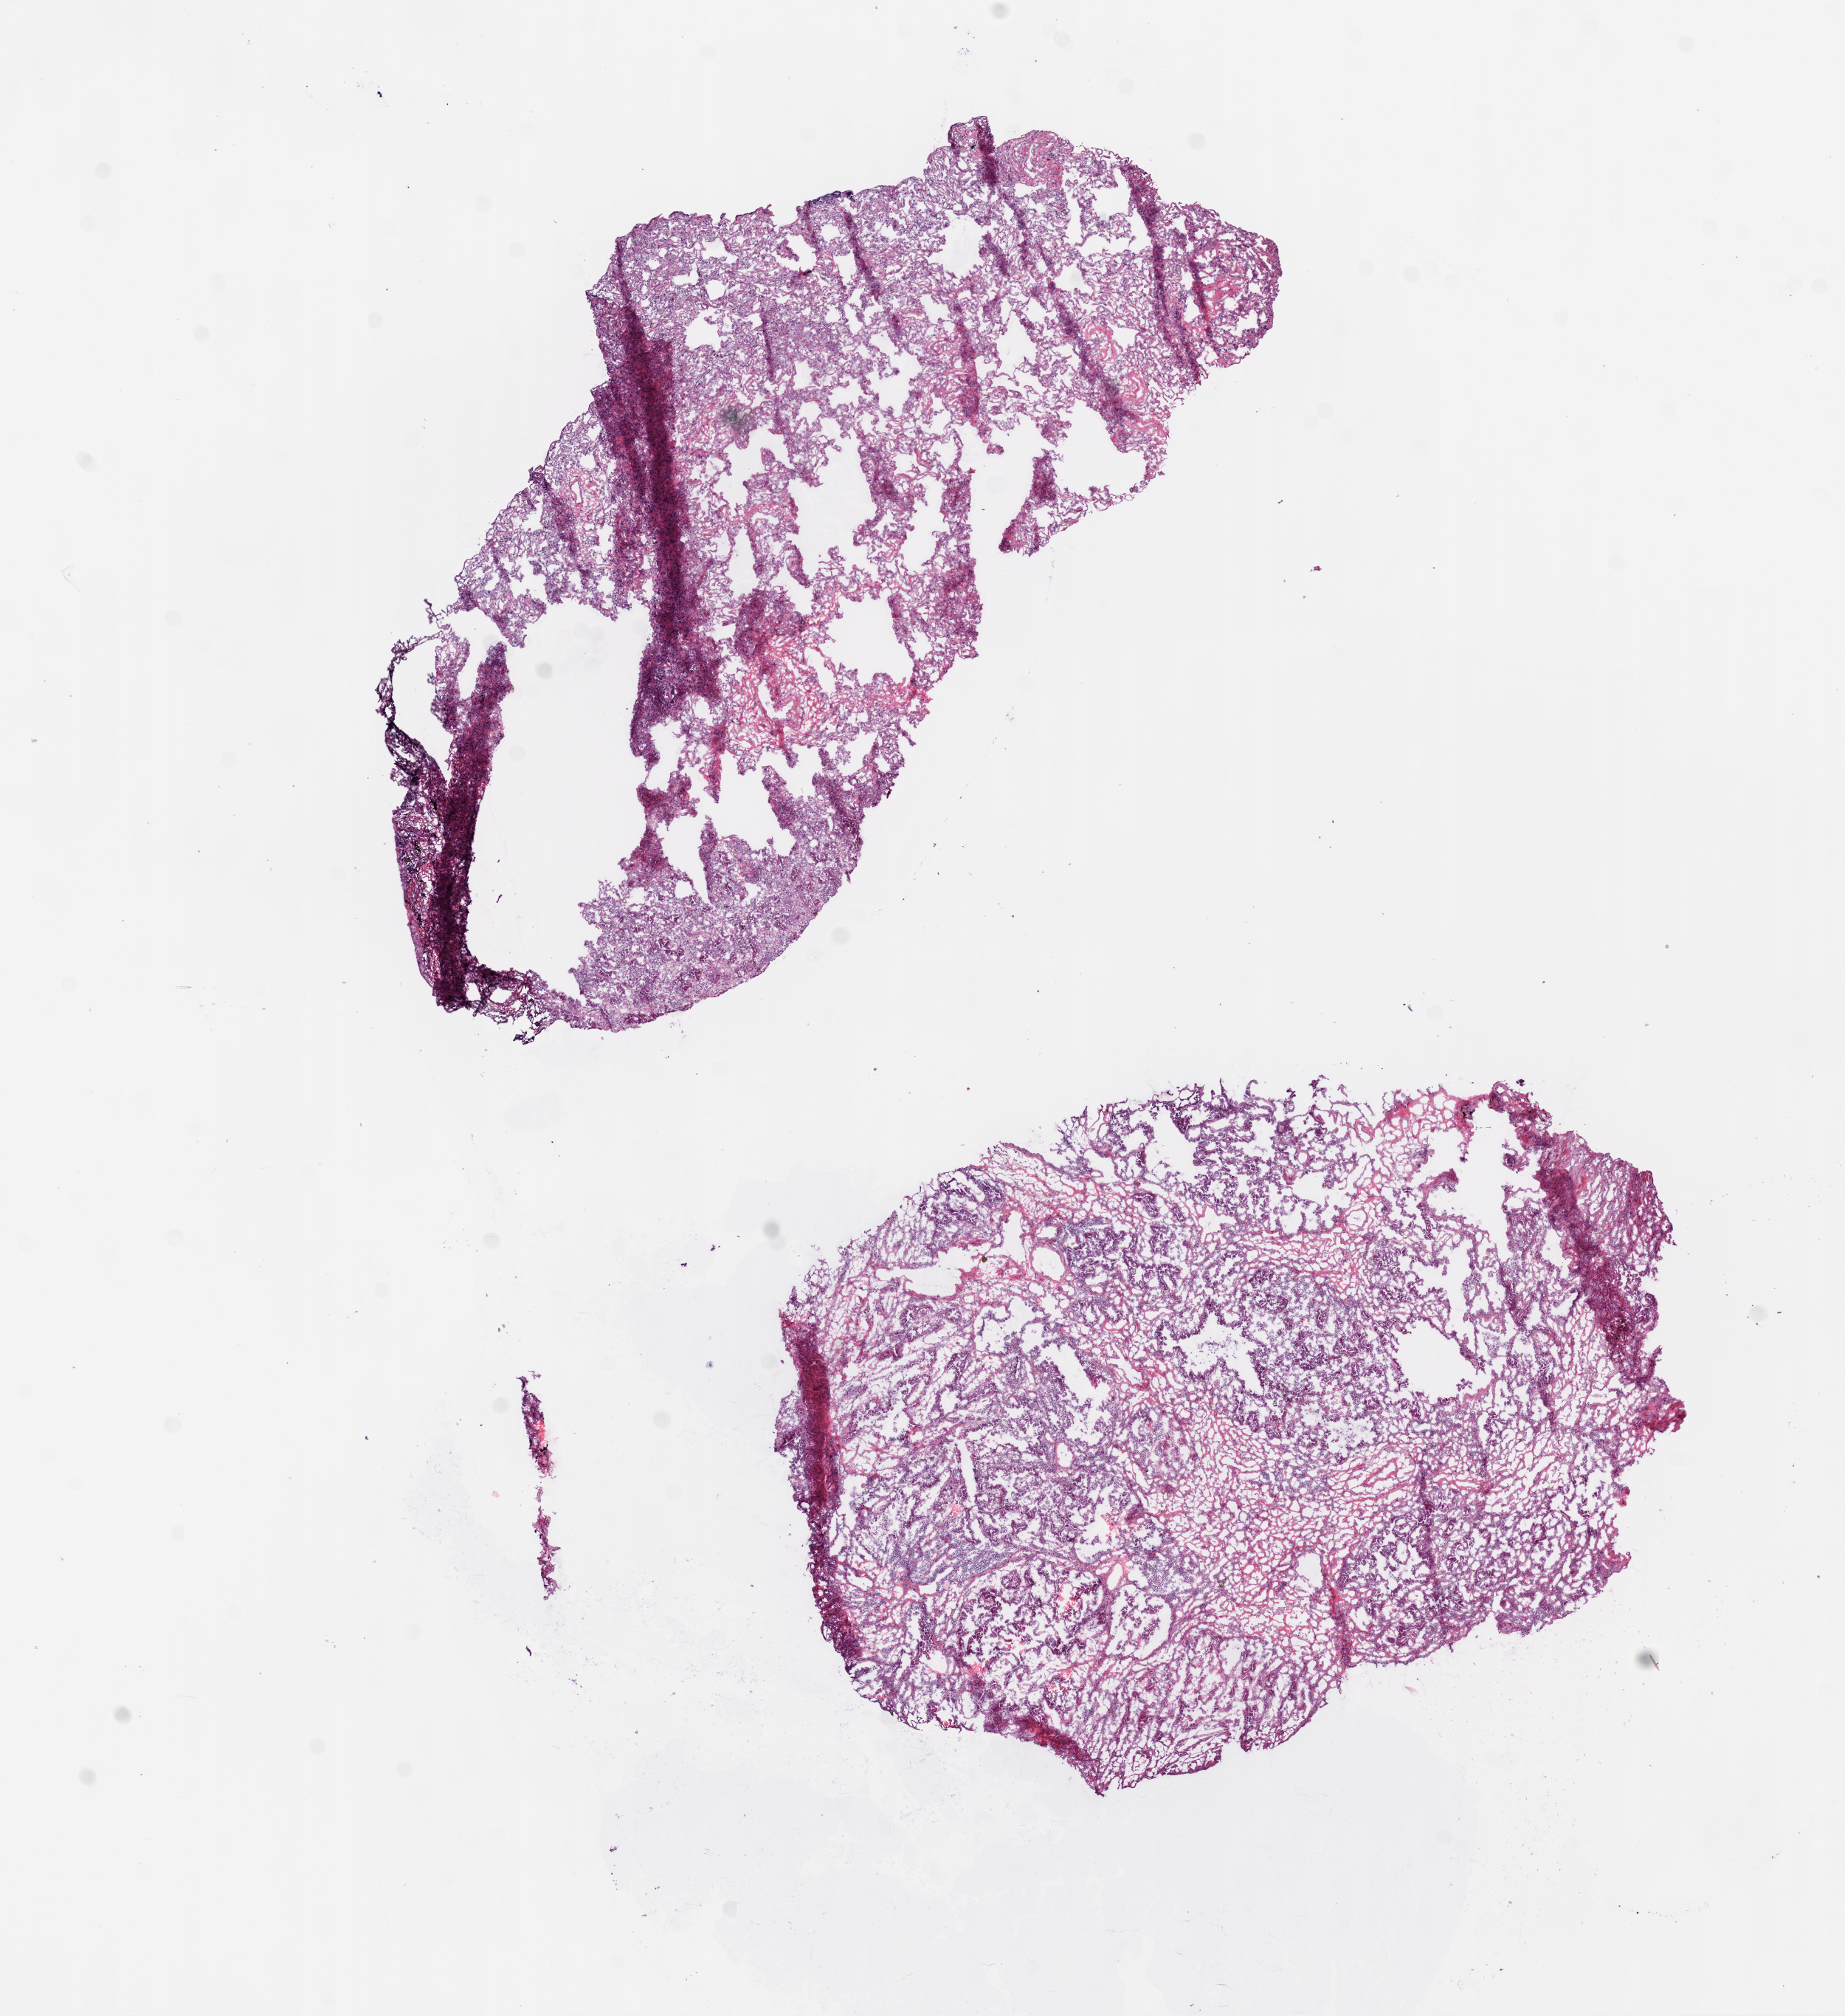
Digitized H&E-stained tissue section (whole slide), whole scanned area (about 10.0 x 11.0 mm, acquisition: 20x scan) shown as a low-resolution overview, frozen section, lung, primary tumour sample. Female, age 65 years at initial diagnosis. Pathologist review of this section (percent, as recorded): tumour cells 60%, tumour nuclei 60%, normal cells 40%, stromal cells 0%, necrosis 0%.
Laterality: right. TNM: T1 N0 M0. Pathologic diagnosis: Adenocarcinoma, NOS. AJCC pathologic stage: IA (6th edition).